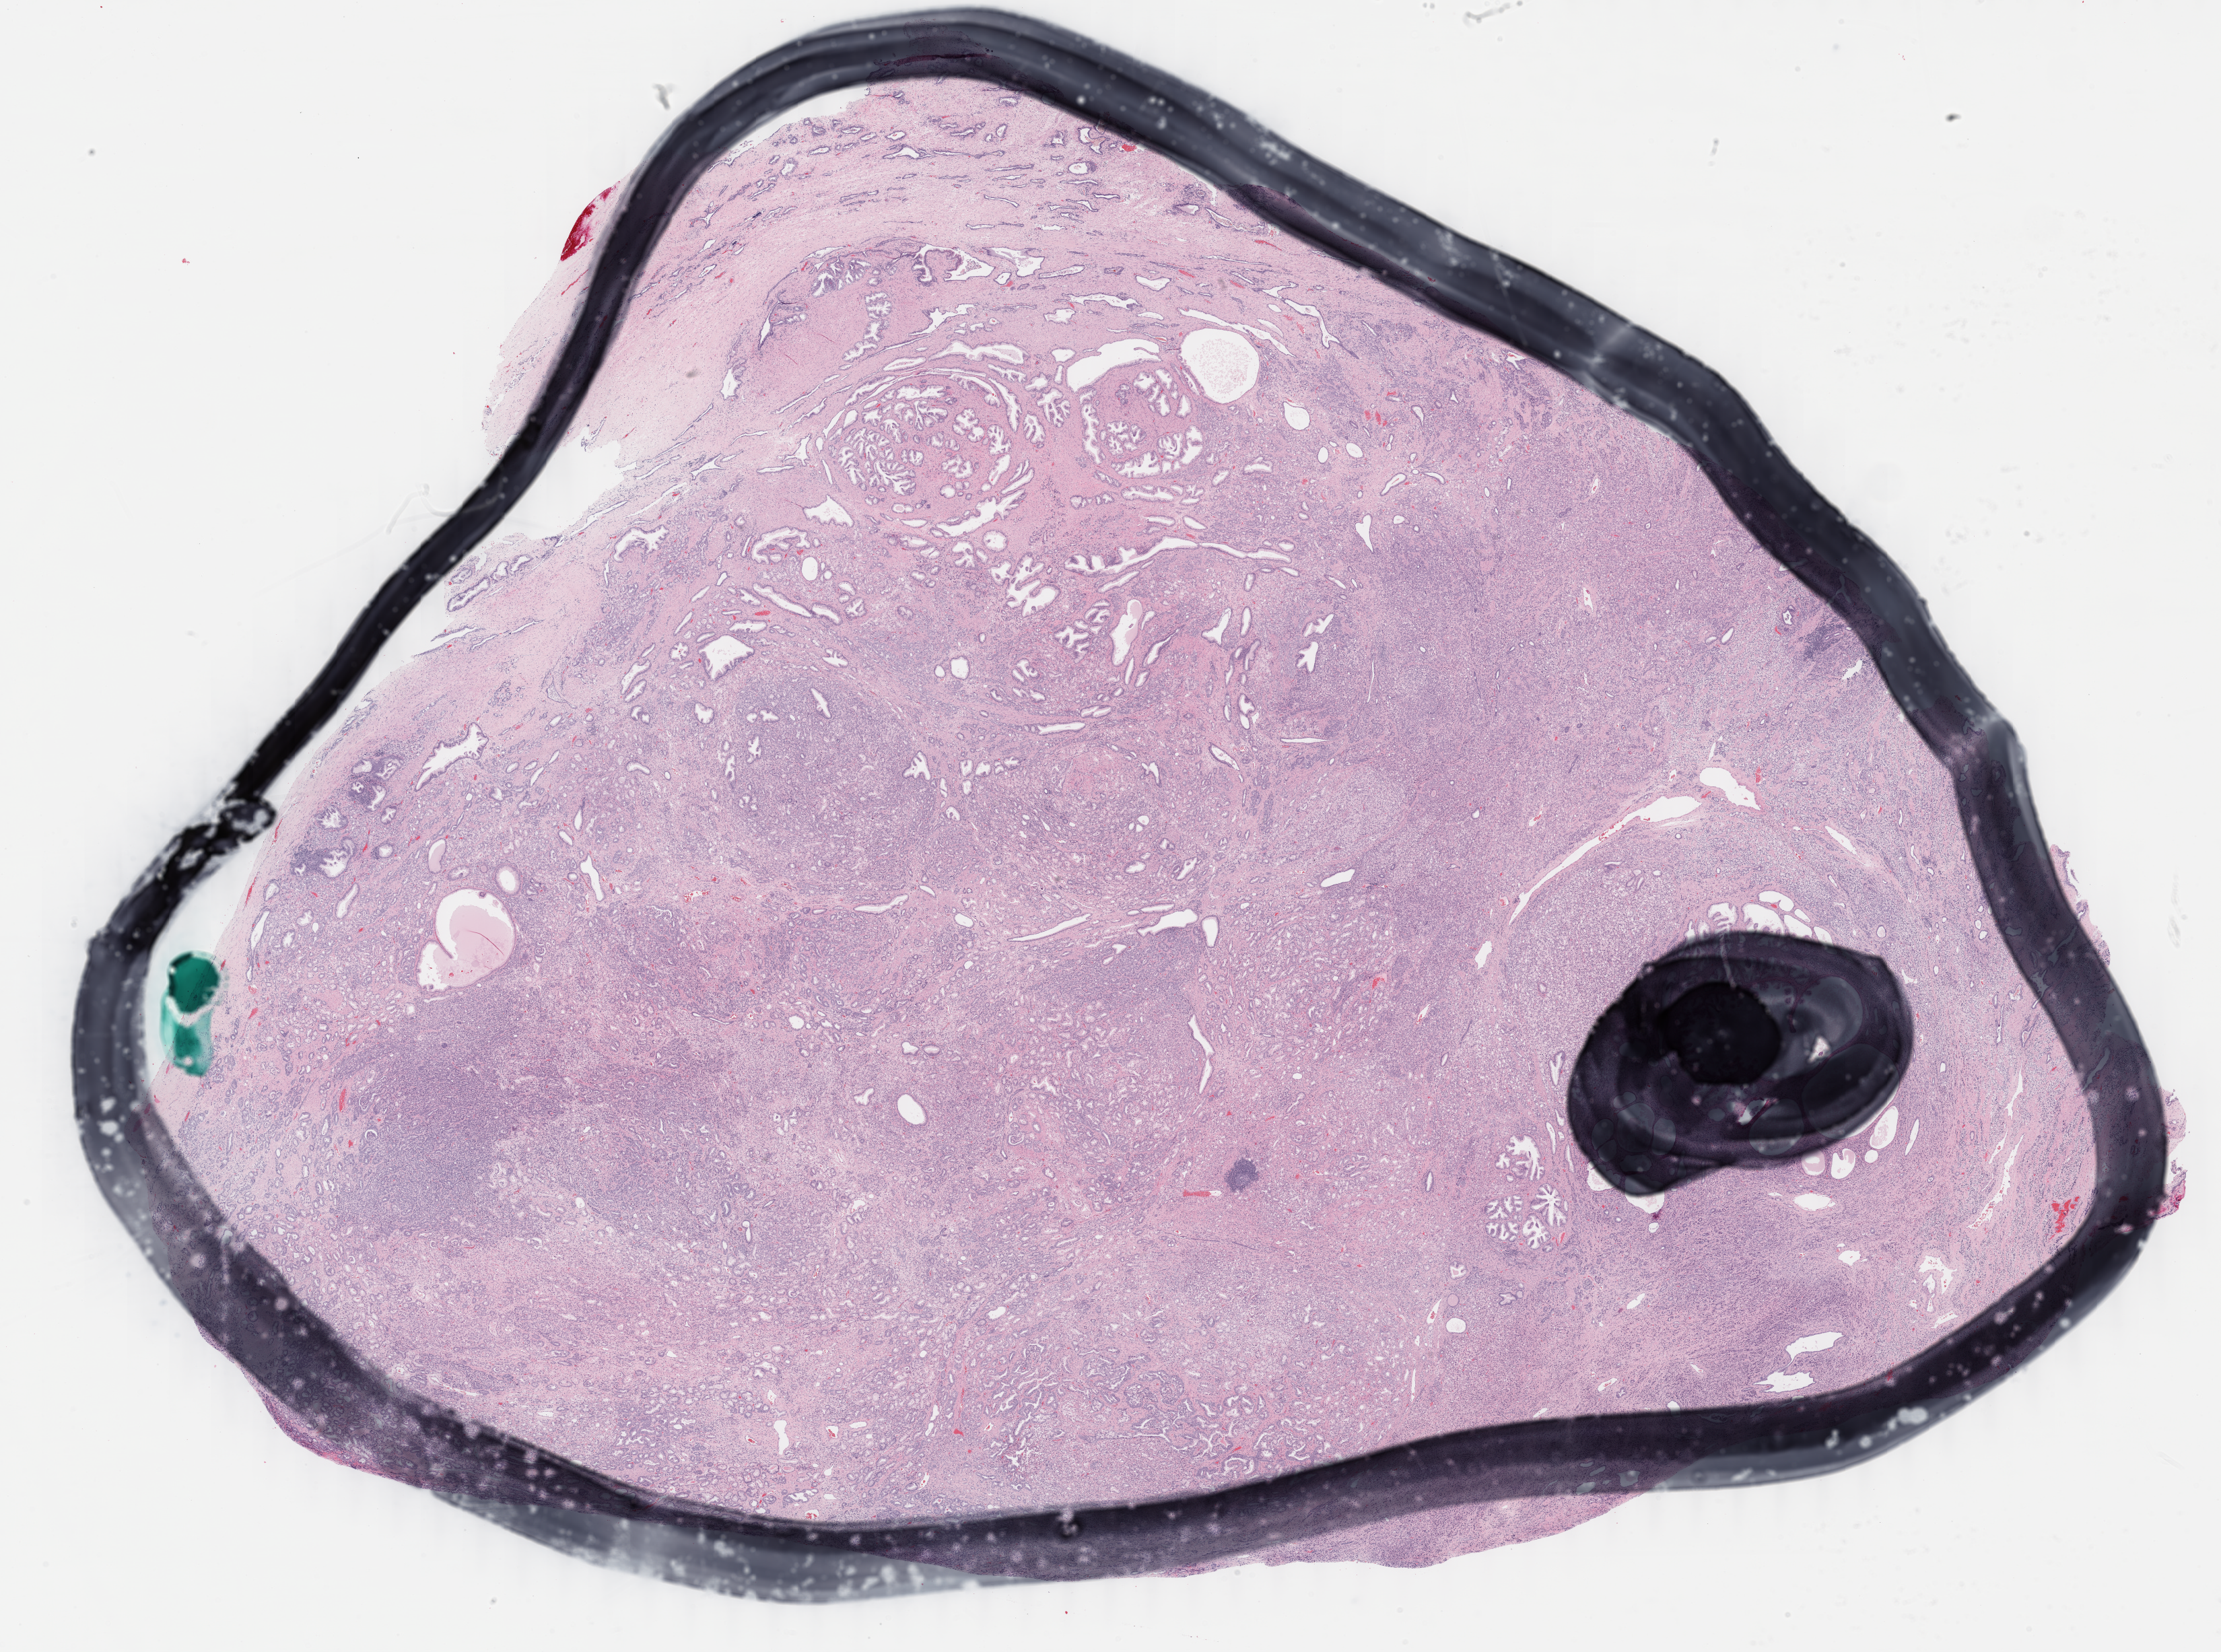
Whole-slide histology image, H&E — a low-resolution overview of the entire scanned area, about 26.2 x 19.5 mm (slide scanned at 40x); formalin-fixed paraffin-embedded (FFPE) diagnostic section; sample: primary tumour, prostate. Male, age 61 years at initial diagnosis. Gleason score: 9 (4+5).
* laterality: bilateral
* lymph nodes positive (case pathology): 0 of 5 examined
* histologic diagnosis: Adenocarcinoma, NOS (prostate gland)